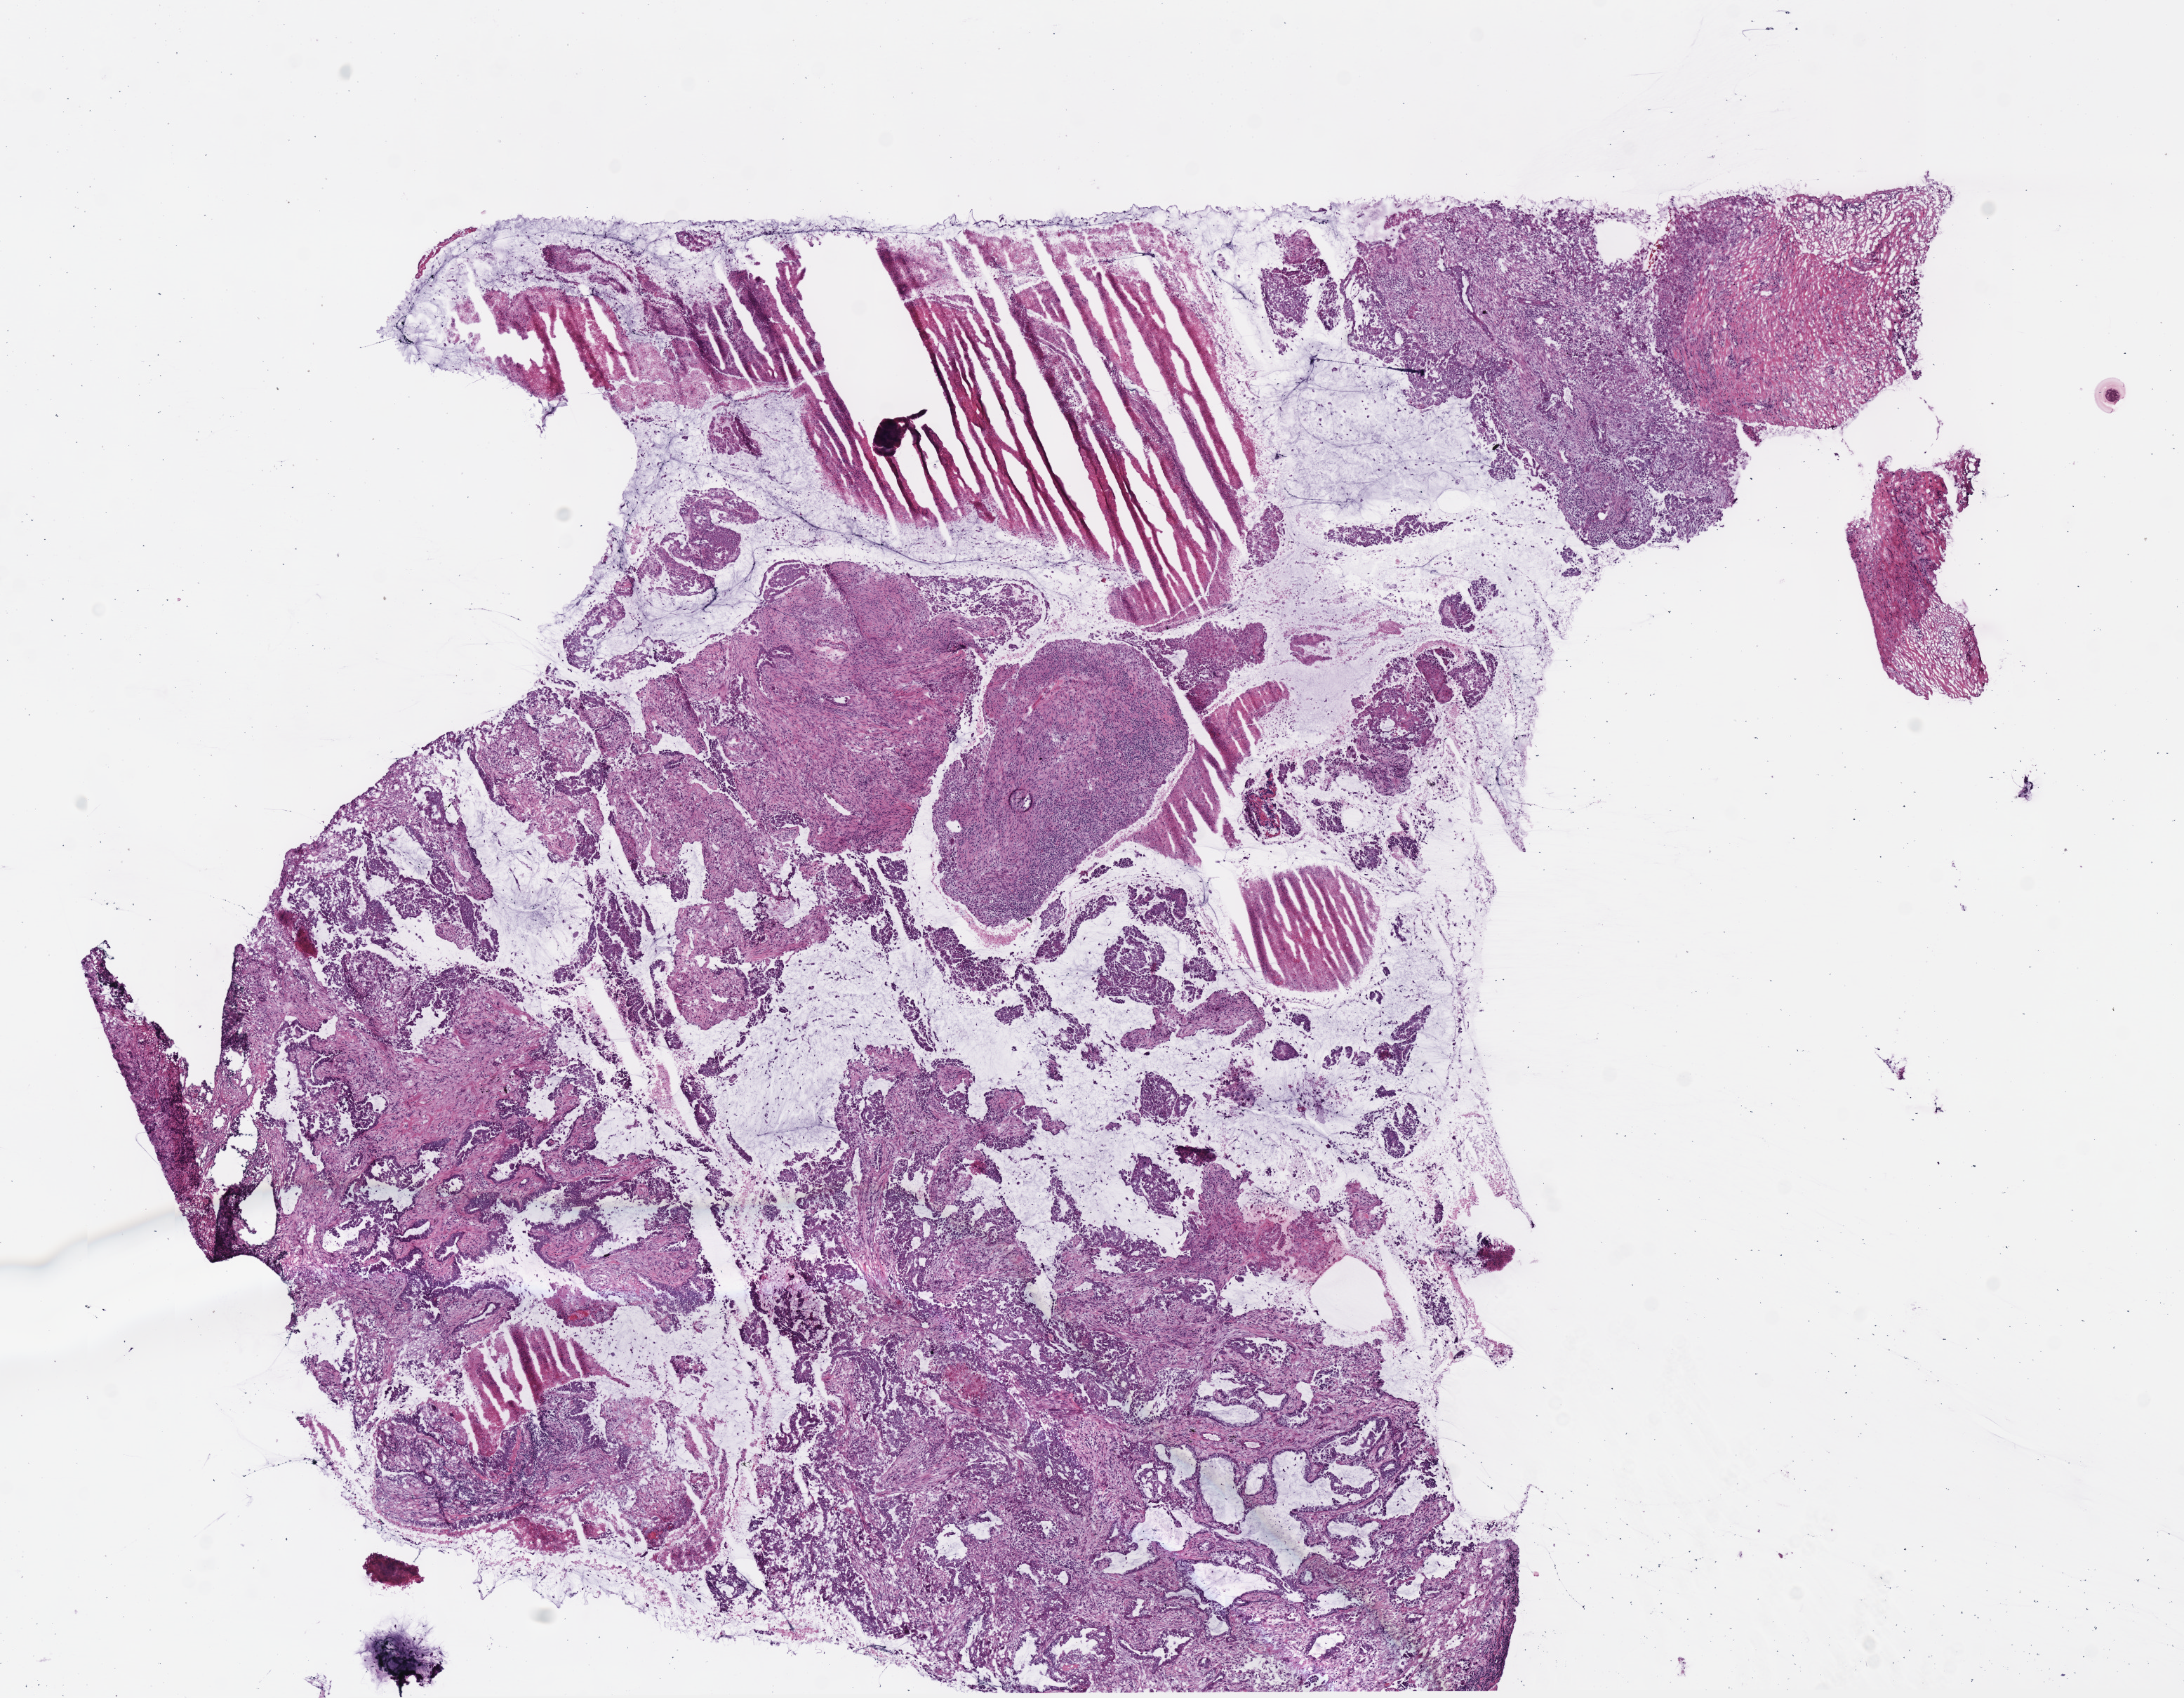
Digitized H&E tissue section (whole slide) — a low-resolution overview of the entire scanned area, about 12.2 x 9.5 mm (slide scanned at 40x), frozen section from the bottom of the tissue portion, primary tumour sample from the lung. Female, age 65 years at initial diagnosis. Slide review estimates, as recorded: tumour cells 68%, tumour nuclei 62%, normal cells 0%, stromal cells 15%, necrosis 17%. Infiltration values recorded for this section: lymphocyte infiltration 20%.
* AJCC pathologic stage: IIA
* TNM: T2a N1 MX
* diagnosis: Adenocarcinoma, NOS
* laterality: left